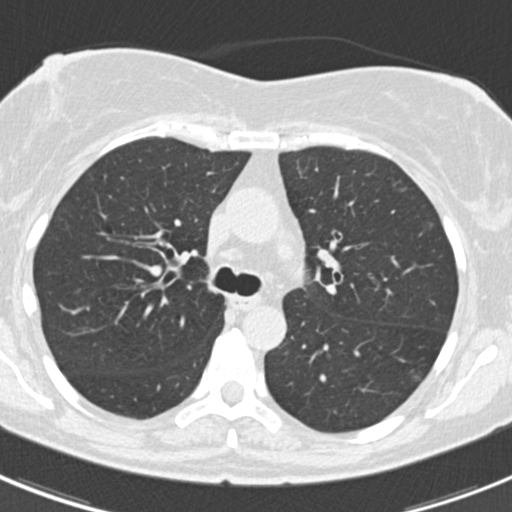
Low-dose screening chest CT, axial slice, first (baseline) screen, lung window (W 1500 / L -600 HU), 2 mm slice thickness, standard (soft-tissue) reconstruction kernel (B30f). Female, age 60 years at enrolment. Current smoker at enrolment.
Expert-annotated lung lesion, box from (x=412, y=215) to (x=443, y=245) px. The screening reader recorded 3 non-calcified nodules or masses ≥4 mm on this exam (lingula, left lower lobe, lingula); which of them this box marks is not recorded. Official screen result: positive, change unspecified: nodule(s) >= 4 mm or enlarging nodule(s), mass(es), or other non-specific abnormalities suspicious for lung cancer. Later outcome: lung cancer diagnosed 886 days after this screen — non-small cell carcinoma, left upper lobe, poorly differentiated (G3), stage IB (AJCC 6th edition), 7 mm at pathology.